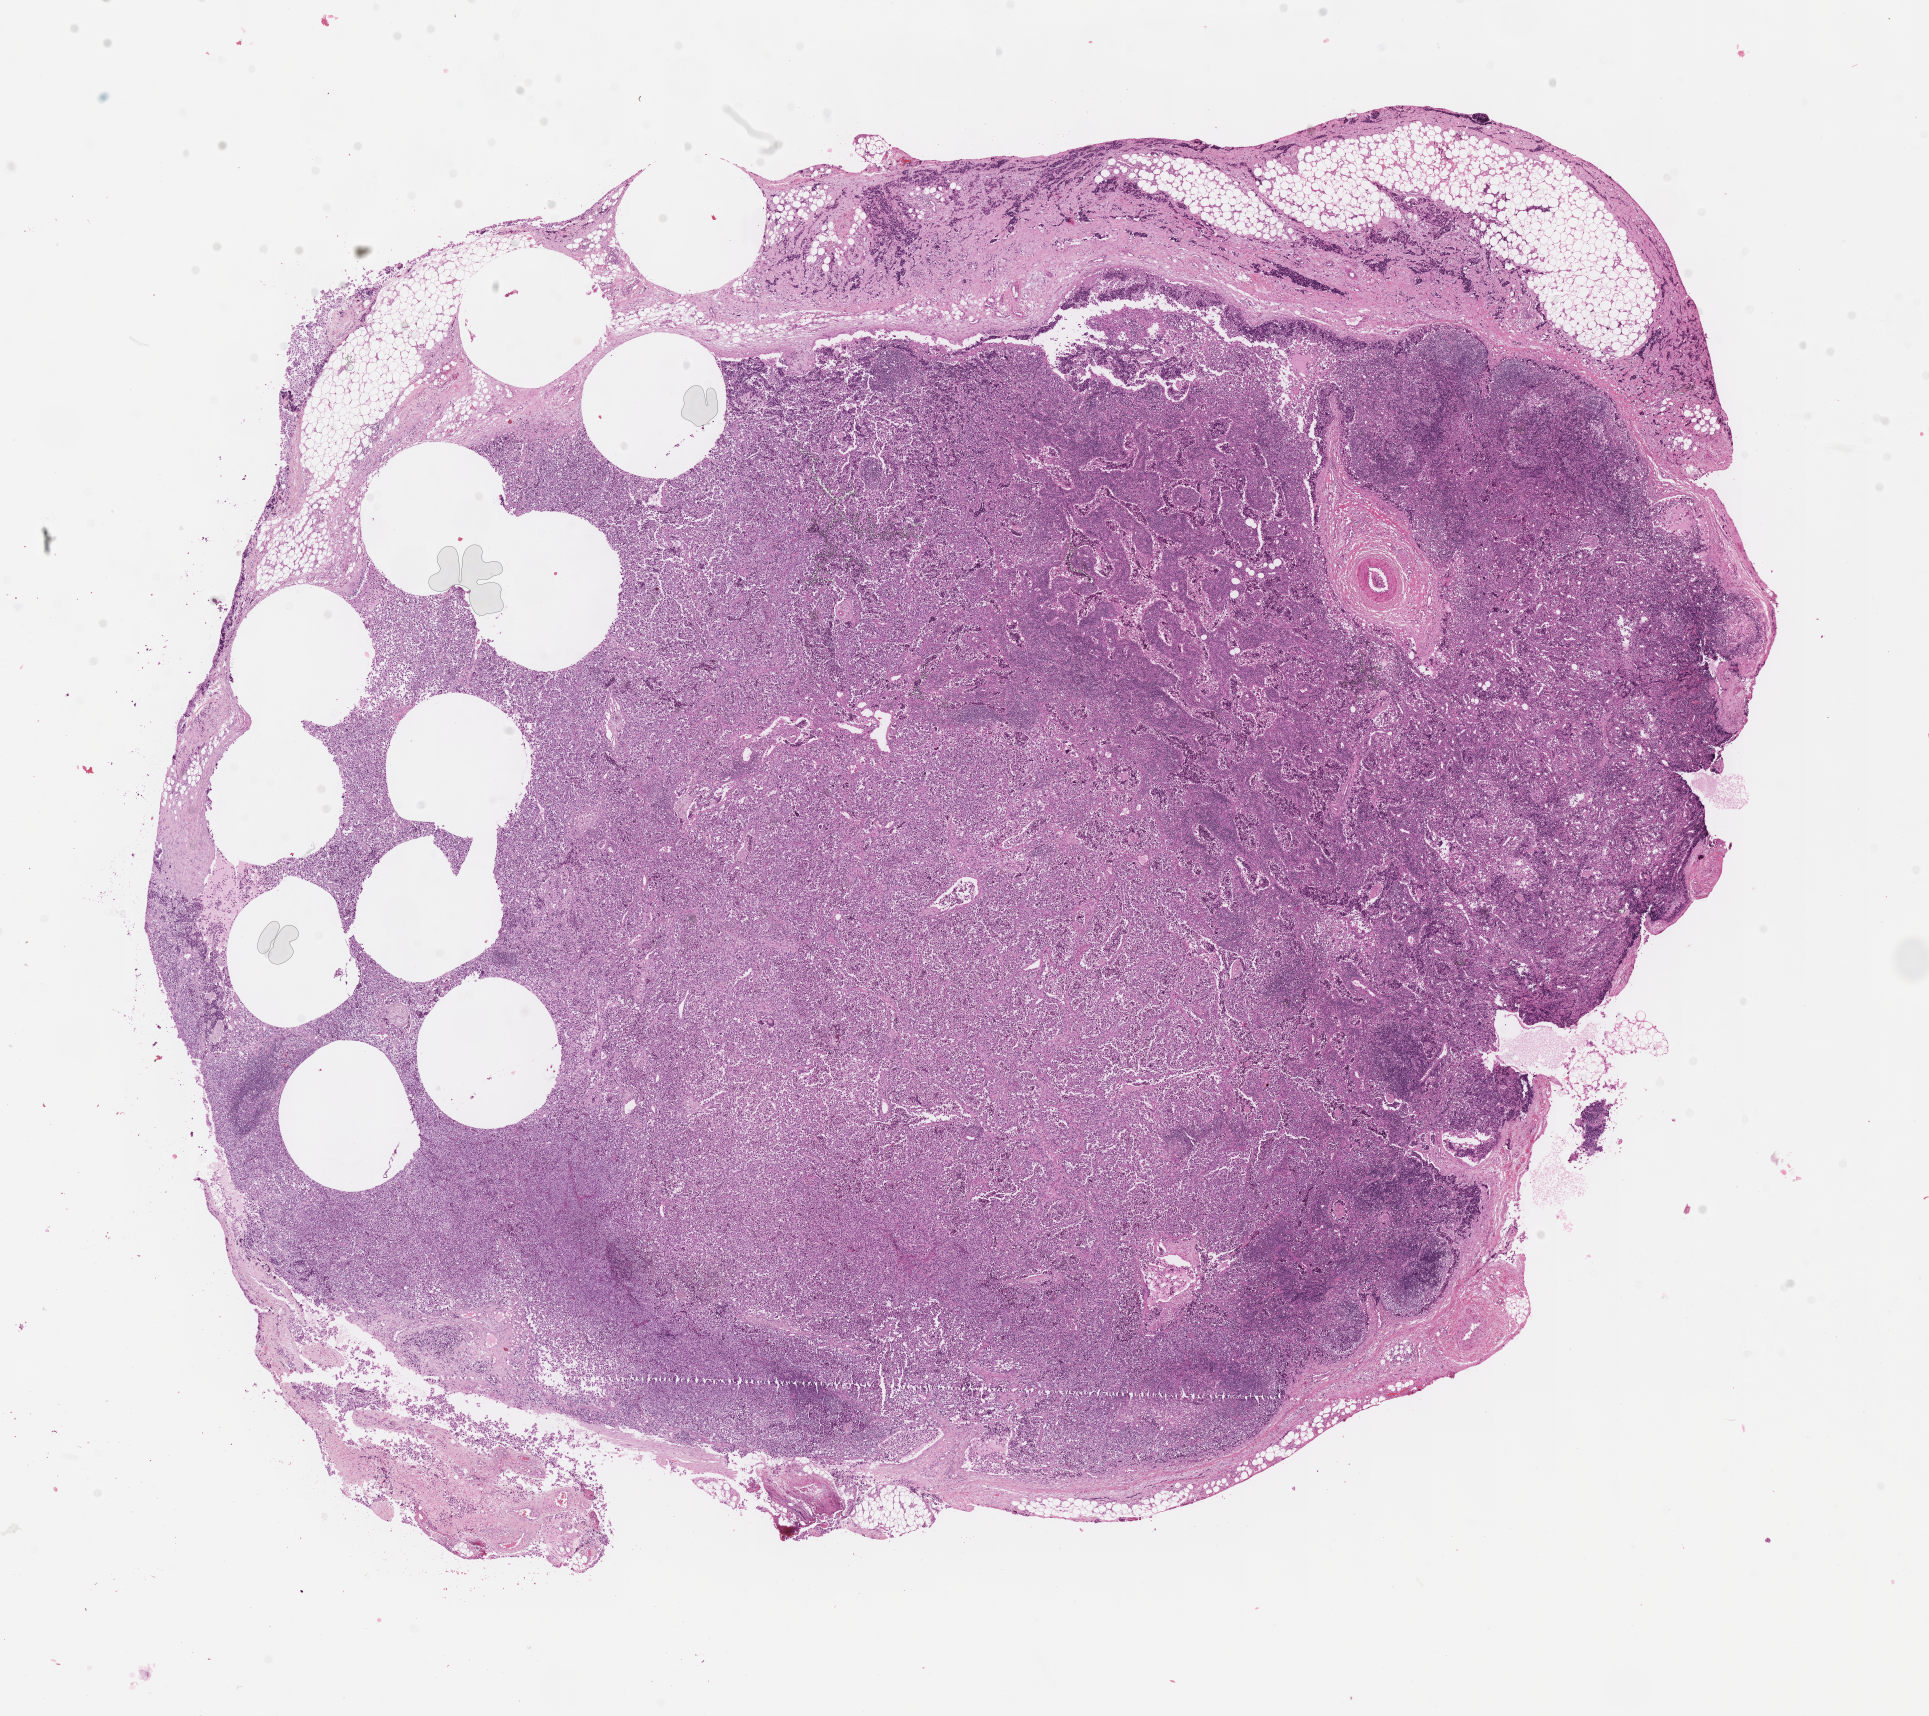
Whole-slide image, haematoxylin and eosin stain of tumor tissue, shown as a low-resolution overview of the whole scanned area (about 15.6 x 13.9 mm), formalin-fixed, paraffin-embedded (FFPE) tissue, site: arm, left. Female patient, age at diagnosis 12.8 years.
Metastatic status at presentation (as recorded): metastatic. Diagnosis: rhabdomyosarcoma; histological classification: alveolar rhabdomyosarcoma. Stage (as recorded): 4.